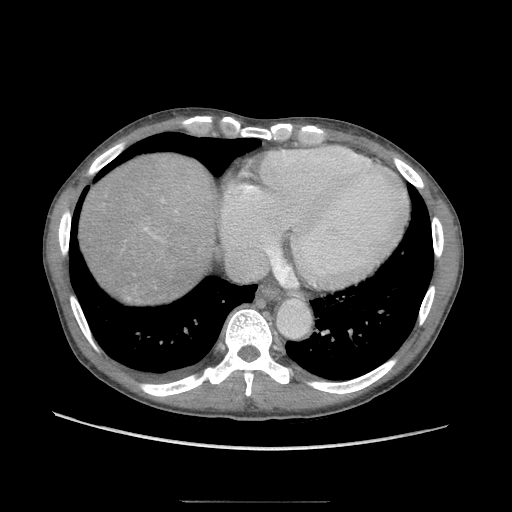
Contrast-enhanced abdominal CT (liver protocol), one axial slice. Slice 91 of 103 in the series (ordered by position). Soft-tissue window (W 400 / L 40 HU). 2.5 mm slice thickness. 512 × 512 image matrix. Case-level facts recorded for this patient, not image findings: diagnosis: hepatocellular carcinoma (patient treated with transarterial chemoembolisation; whether this scan precedes or follows treatment is not stated here); TNM stage (as recorded): Stage-IIIA; Child-Pugh class: A; tumour differentiation: moderately differentiated; tumour nodularity: multinodular.
Outlined on this slice (semi-automatic segmentation, software-assisted and operator-edited):
- abdominal aorta: bounding box <278,300,310,336> (left, top, right, bottom; pixels)
- liver parenchyma outside the tumour (the mass and vessels are separate outlines, so this box may not span the whole liver): <82,154,214,296>